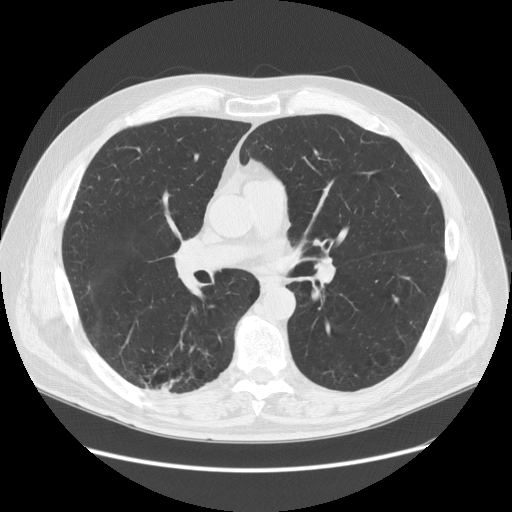
Low-dose screening chest CT, one axial slice. Position 79 of 149 along the scan axis. Lung window (W 1500 / L -600 HU). 2.5 mm slice thickness. 512 × 512 image matrix, field of view 400 × 400 mm.
Outlined on this slice (outlined manually by an expert reader):
- lesion 1 (tumor, lower lobe of right lung): bounding box [x1, y1, x2, y2] px = [161, 380, 179, 390]